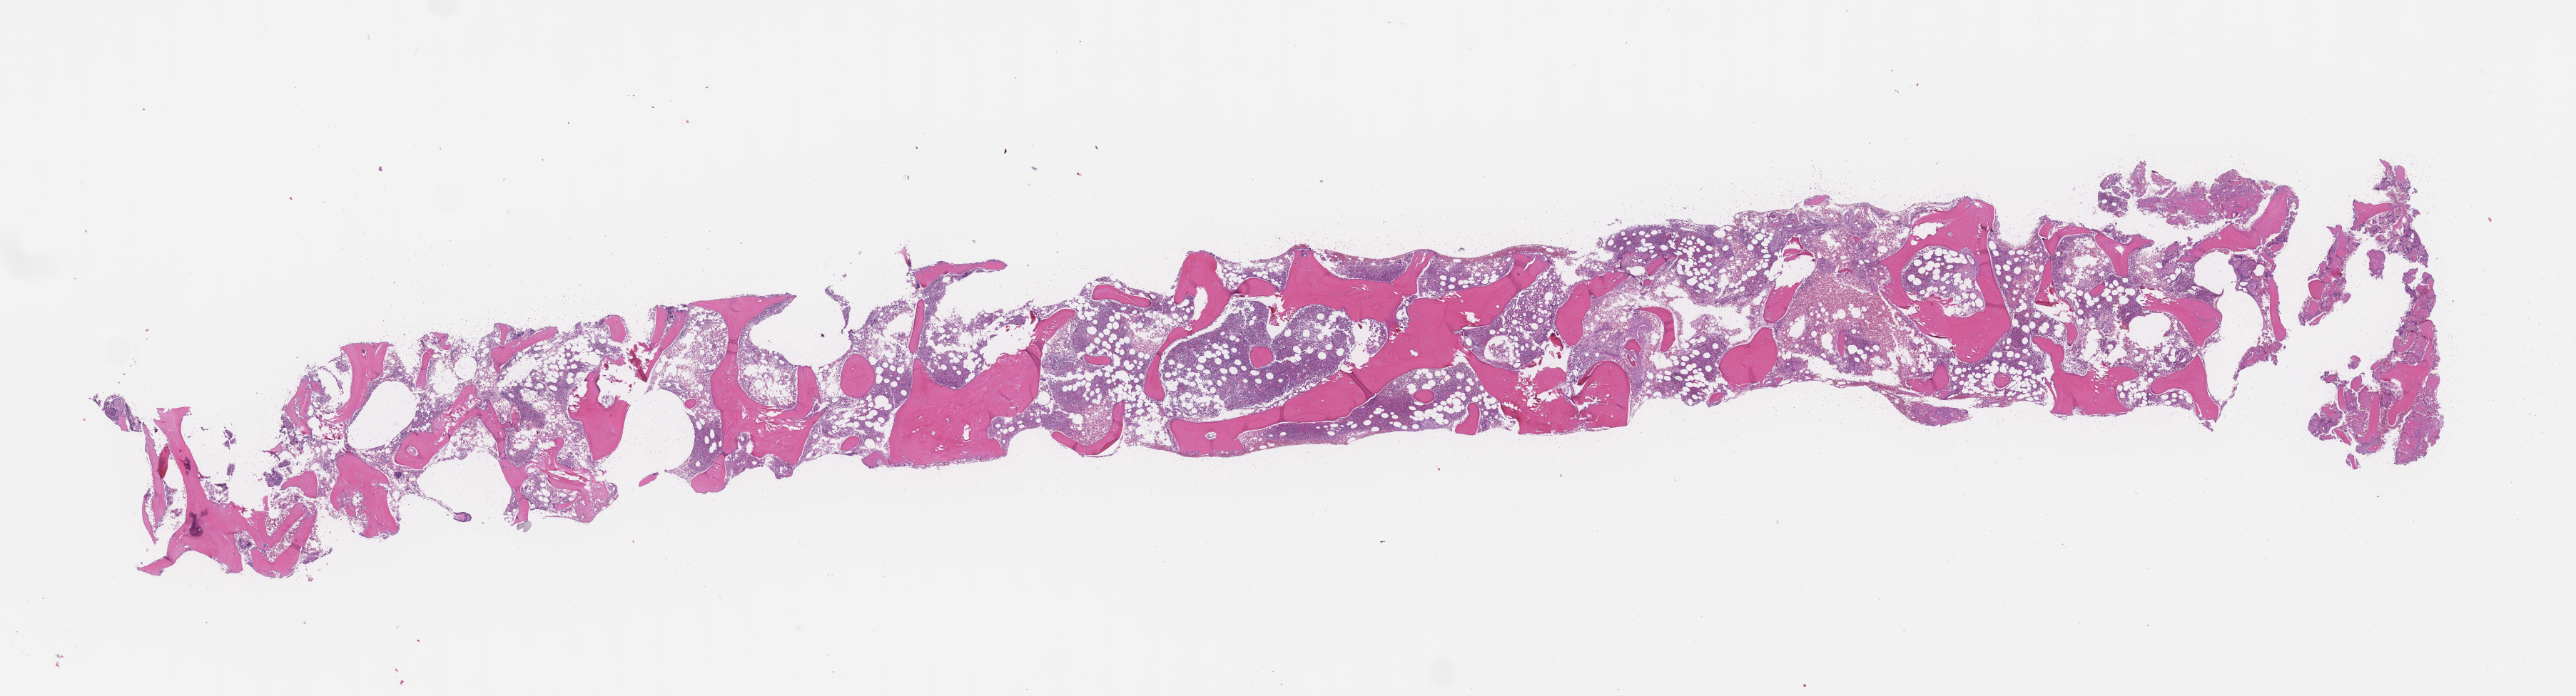
Whole-slide image, hematoxylin and eosin (H&E) stain, whole scanned area (about 29.1 x 7.9 mm) shown as a low-resolution overview. Formalin-fixed, paraffin-embedded (FFPE) tissue. Site: bone marrow. Archival tissue. Patient: female.
This section: primary tumor. Diagnosis: Plasma Cell Myeloma.